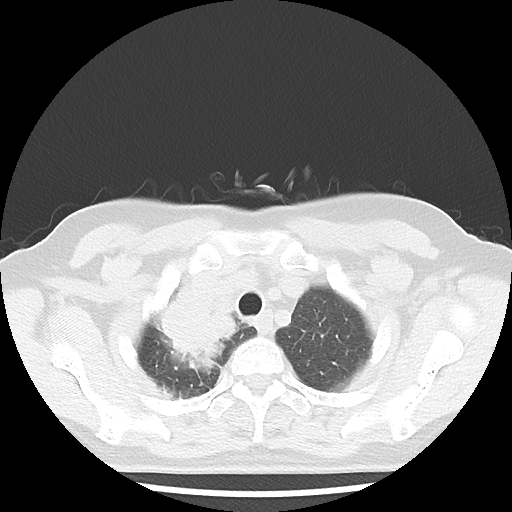
Chest CT, one axial slice; position 37 of 43 along the scan axis; reconstruction kernel LUNG; 100 kVp; lung window (W 1500 / L -600 HU); 5 mm slice thickness; 512 × 512 image matrix. Patient: female, 62 years. From the clinical record (not read from this slice): clinical TNM (as recorded): T3 N0 M0; histopathological grade: G3.
Annotated regions visible in this slice (bounding box drawn by a radiologist):
- lung tumour (recorded histology: small cell carcinoma): bounding box [x1, y1, x2, y2] px = [150, 269, 252, 377]